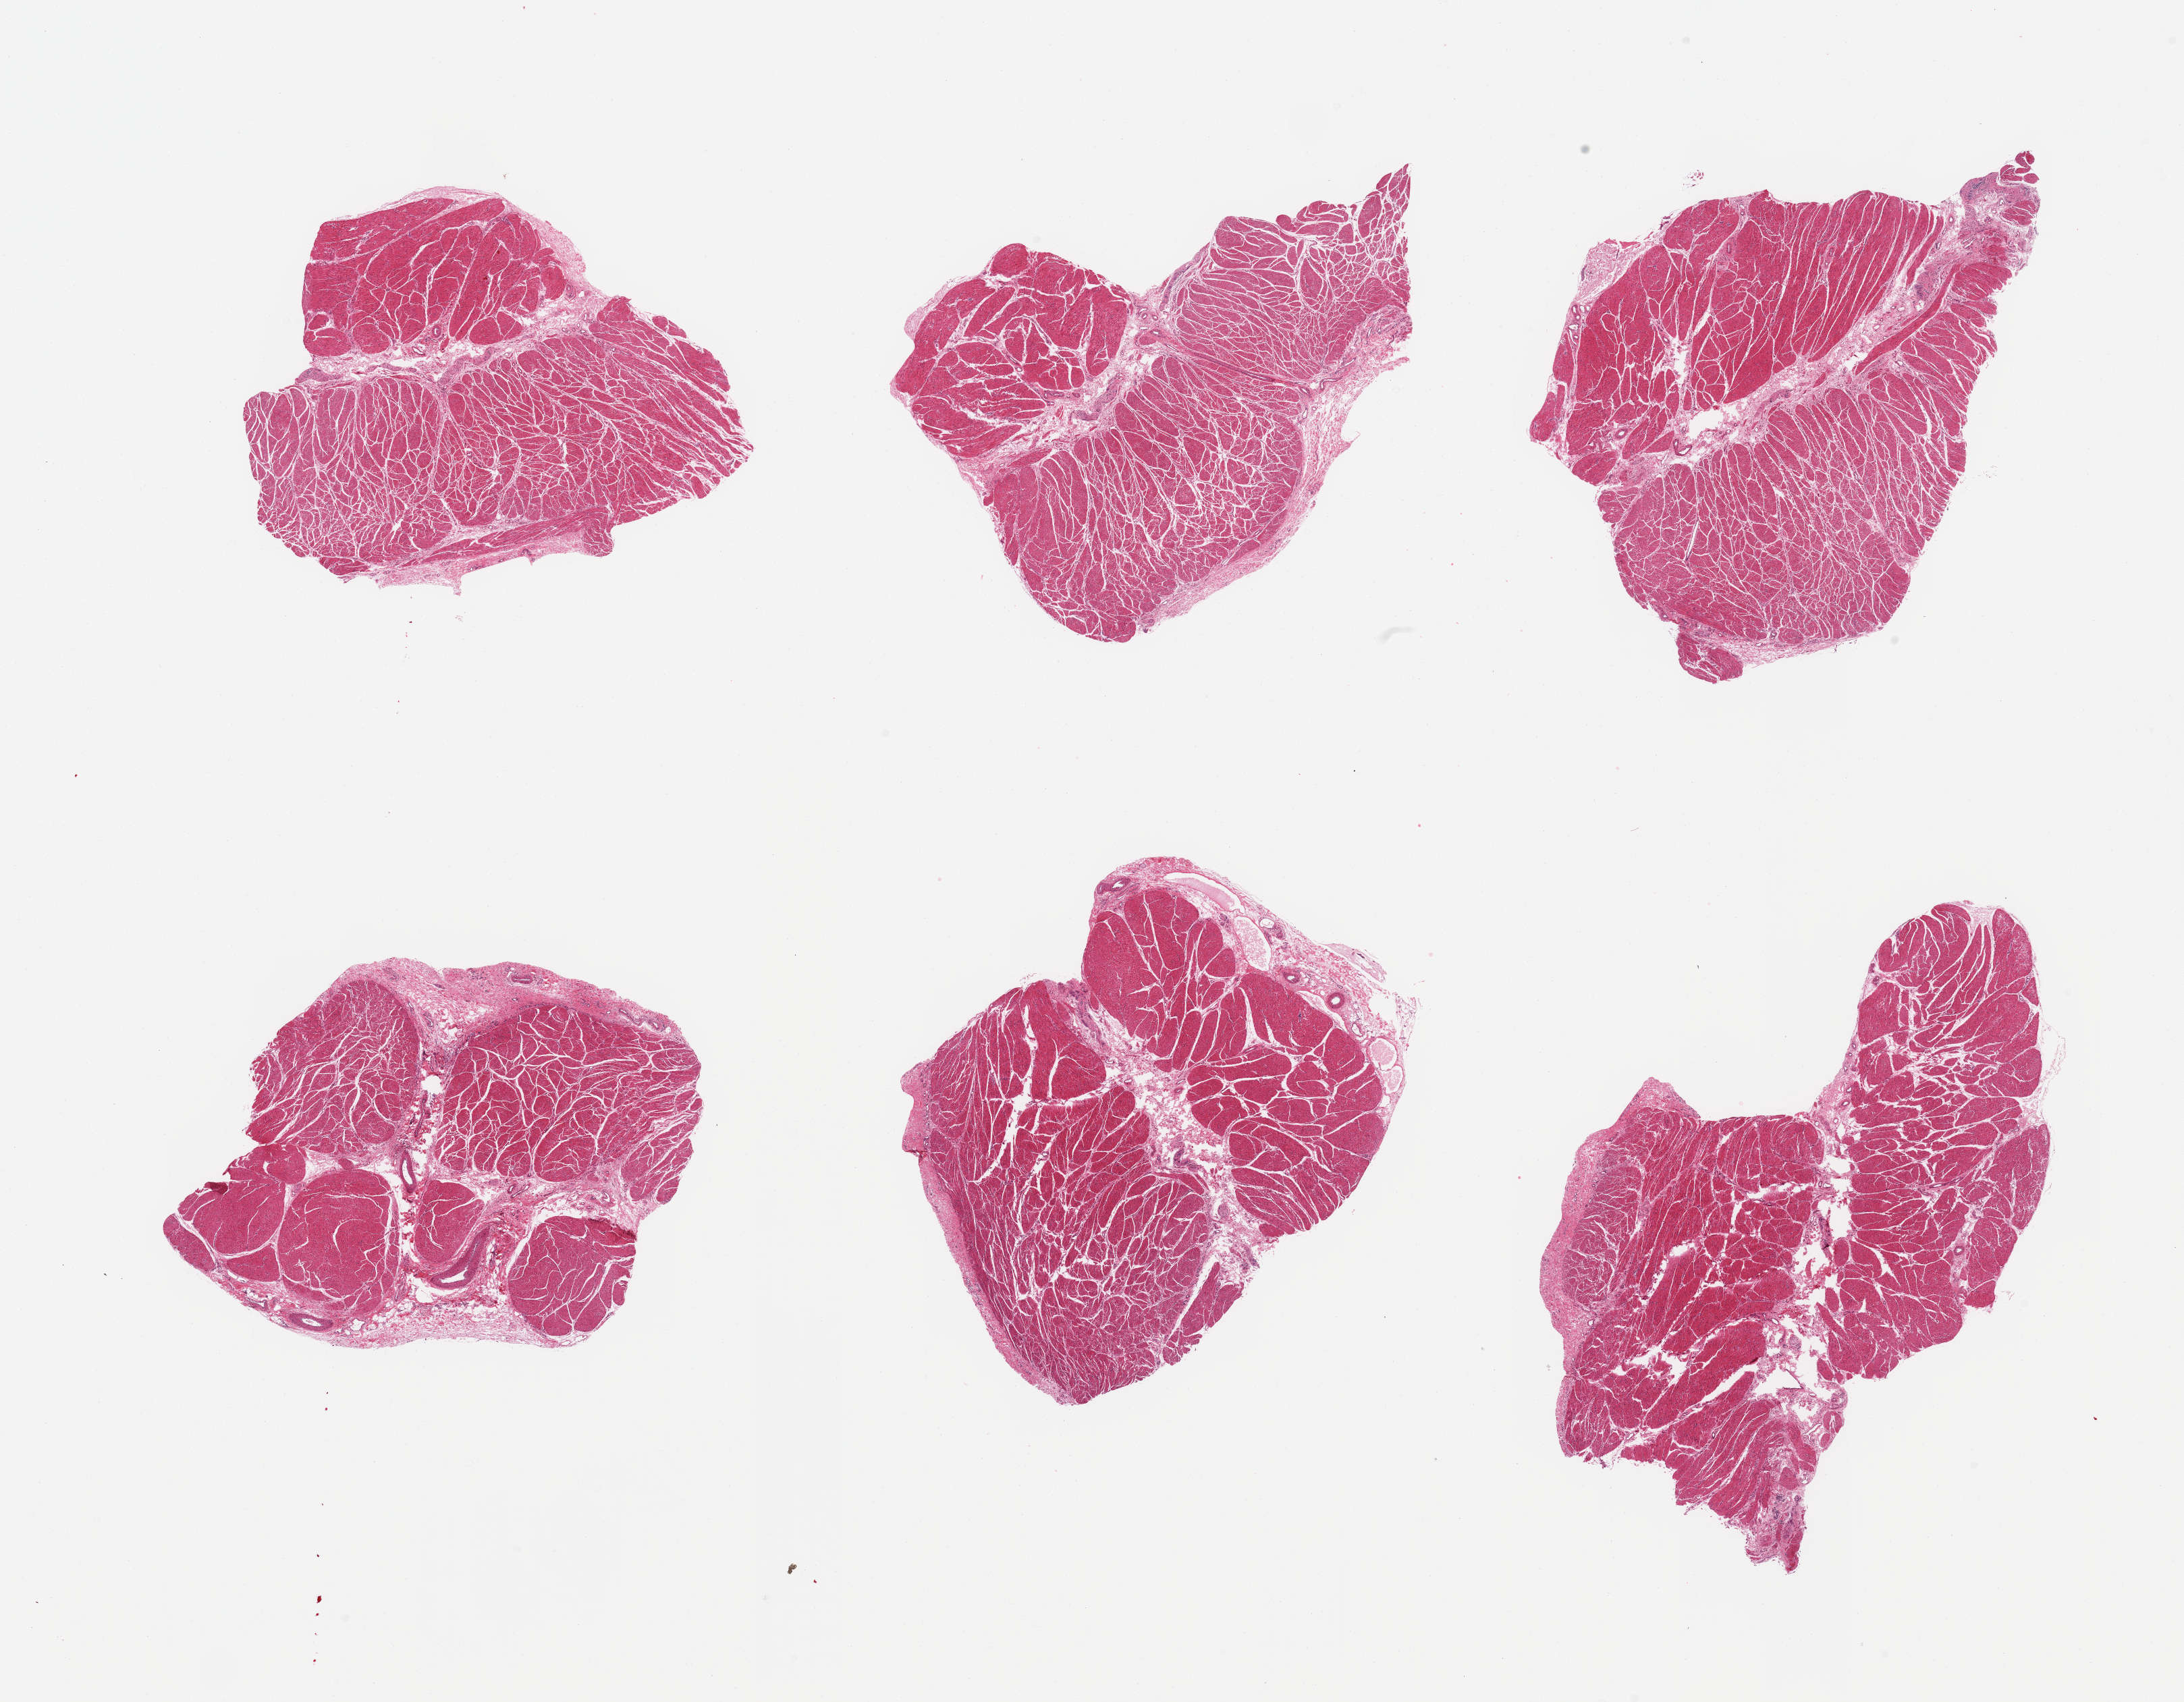
Digitized hematoxylin and eosin (H&E)-stained section, brightfield, a low-resolution overview of the entire scanned area, about 25.6 x 19.9 mm. PAXgene-fixed paraffin-embedded (PFPE) section. Sampled site (target tissue): gastroesophageal junction. Tissue donor sample. Donor sex: male.
* review note (as recorded): 6 pieces; target muscularis with rim of serosa and perimysium with ganglions, nerves and vessels